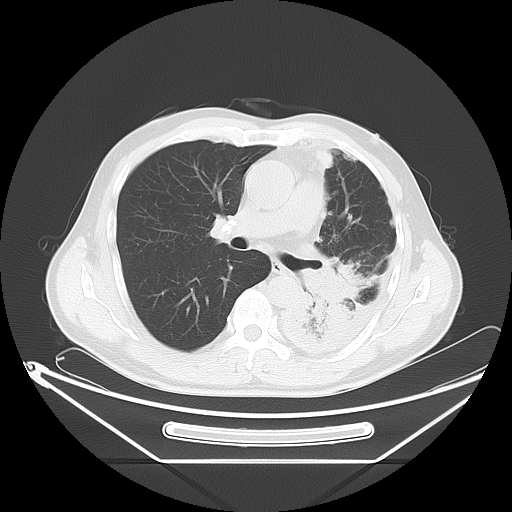
Chest CT, one axial slice; lung window (W 1500 / L -600 HU); 5 mm slice thickness; 512 × 512 image matrix, field of view 442 × 442 mm. Patient: male, 60 years. Case-level facts recorded for this patient, not image findings: clinical TNM (as recorded): T4 N1 M1.
Annotated regions visible in this slice (rectangle marked by the reading radiologist):
- lung tumour (recorded histology: adenocarcinoma): bounding box (x1, y1, x2, y2) in pixels: (295, 246, 374, 322)